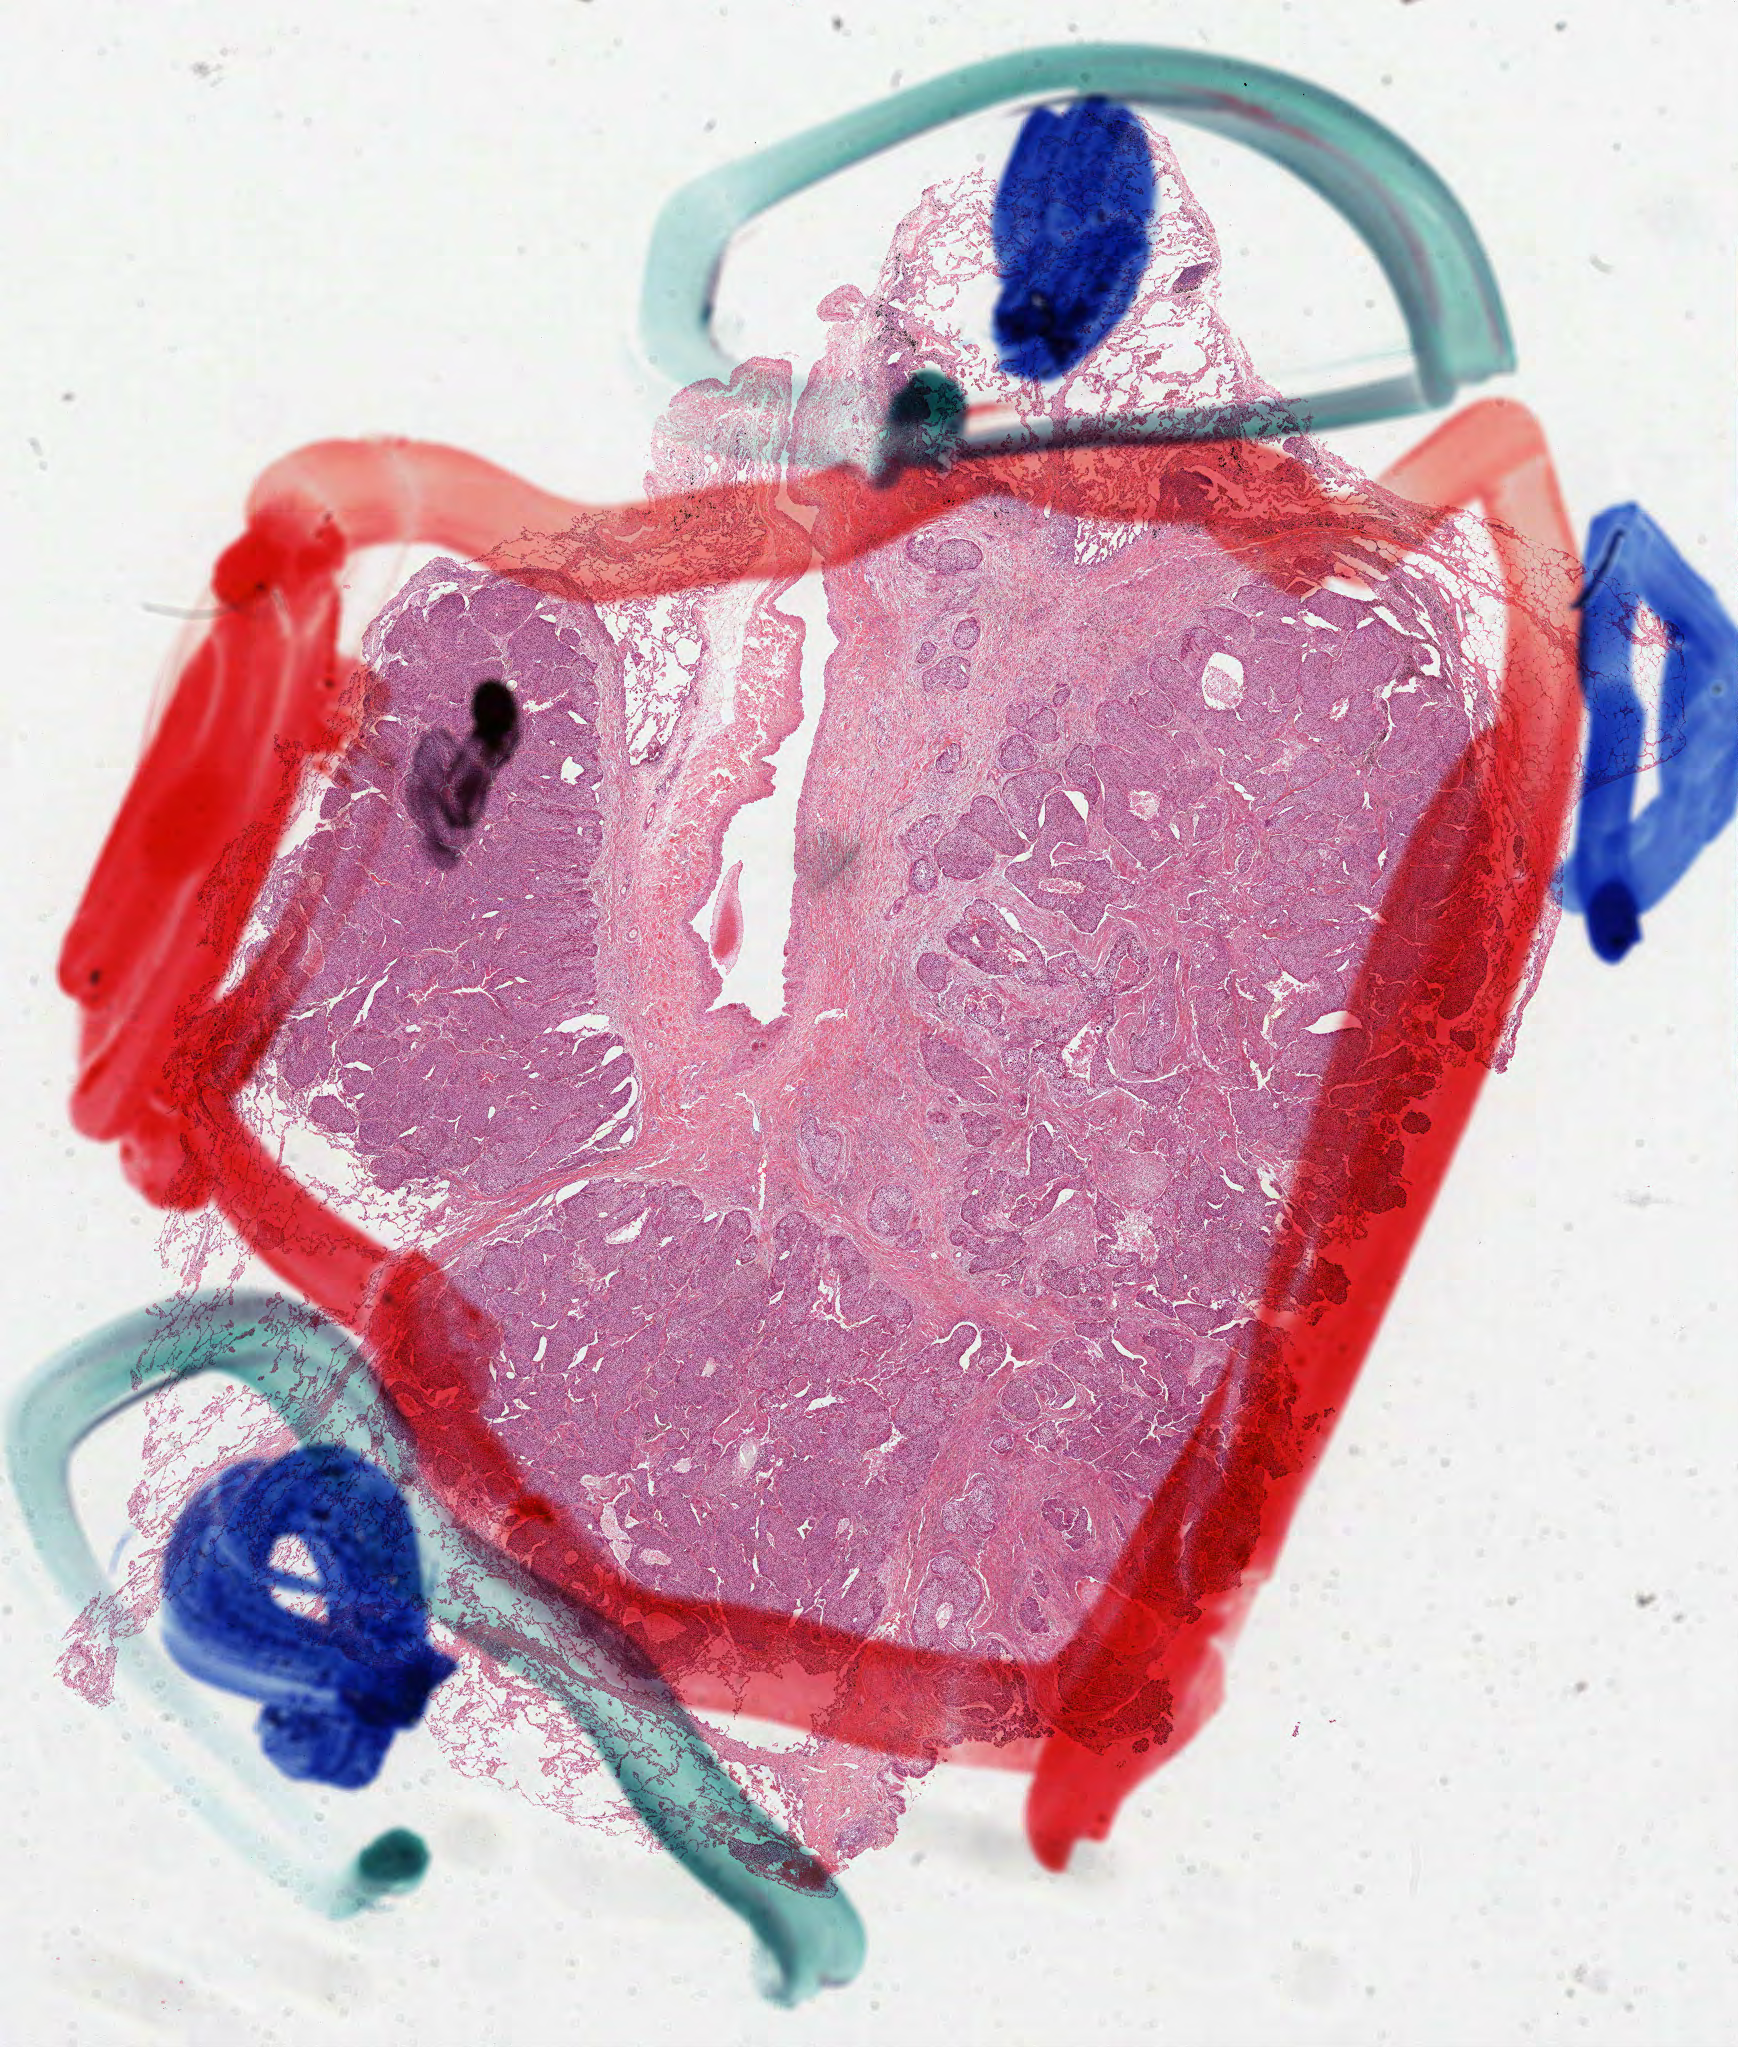
H&E-stained whole-slide image — a low-resolution overview of the entire scanned area, about 14.0 x 16.5 mm. FFPE section. Primary tumour sample from the lung. Male patient; age at initial diagnosis 64 years.
Pathologic diagnosis: Squamous cell carcinoma, NOS (upper lobe, lung). Laterality: left. AJCC pathologic stage: IA (7th edition).